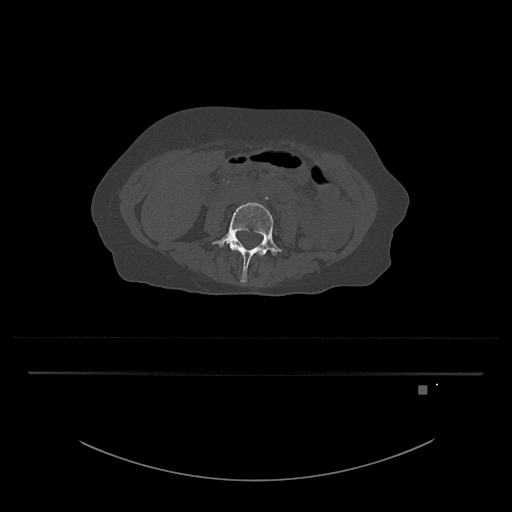
CT including the spine, one axial slice. Slice 366 of 797 in the series (ordered by position). Reconstruction kernel Br40s/3. Bone window (W 1800 / L 400 HU). 512 × 512 image matrix. Patient: female, 57 years. From the clinical record (not read from this slice): primary cancer: cervical.
Outlined on this slice (semi-automatically segmented with operator editing):
- L3 vertebra: bounding box (x1, y1, x2, y2) in pixels: (259, 254, 262, 256)
- L4 vertebra: (212, 202, 282, 282)